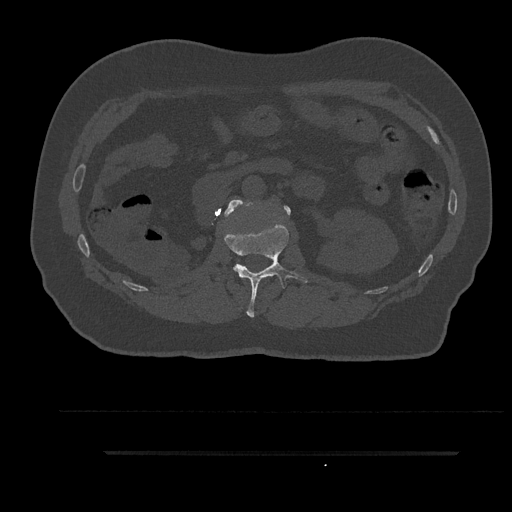
CT including the spine, one axial slice. Position 162 of 797 along the scan axis. 120 kVp. Bone window (W 1800 / L 400 HU). 512 × 512 image matrix, field of view 432 × 432 mm. Patient: male, 63 years. From the clinical record (not read from this slice): primary cancer: renal.
Outlined on this slice (semi-automatically segmented with operator editing):
- L1 vertebra: bounding box <225,223,308,318> (left, top, right, bottom; pixels)
- L2 vertebra: <224,199,291,216>